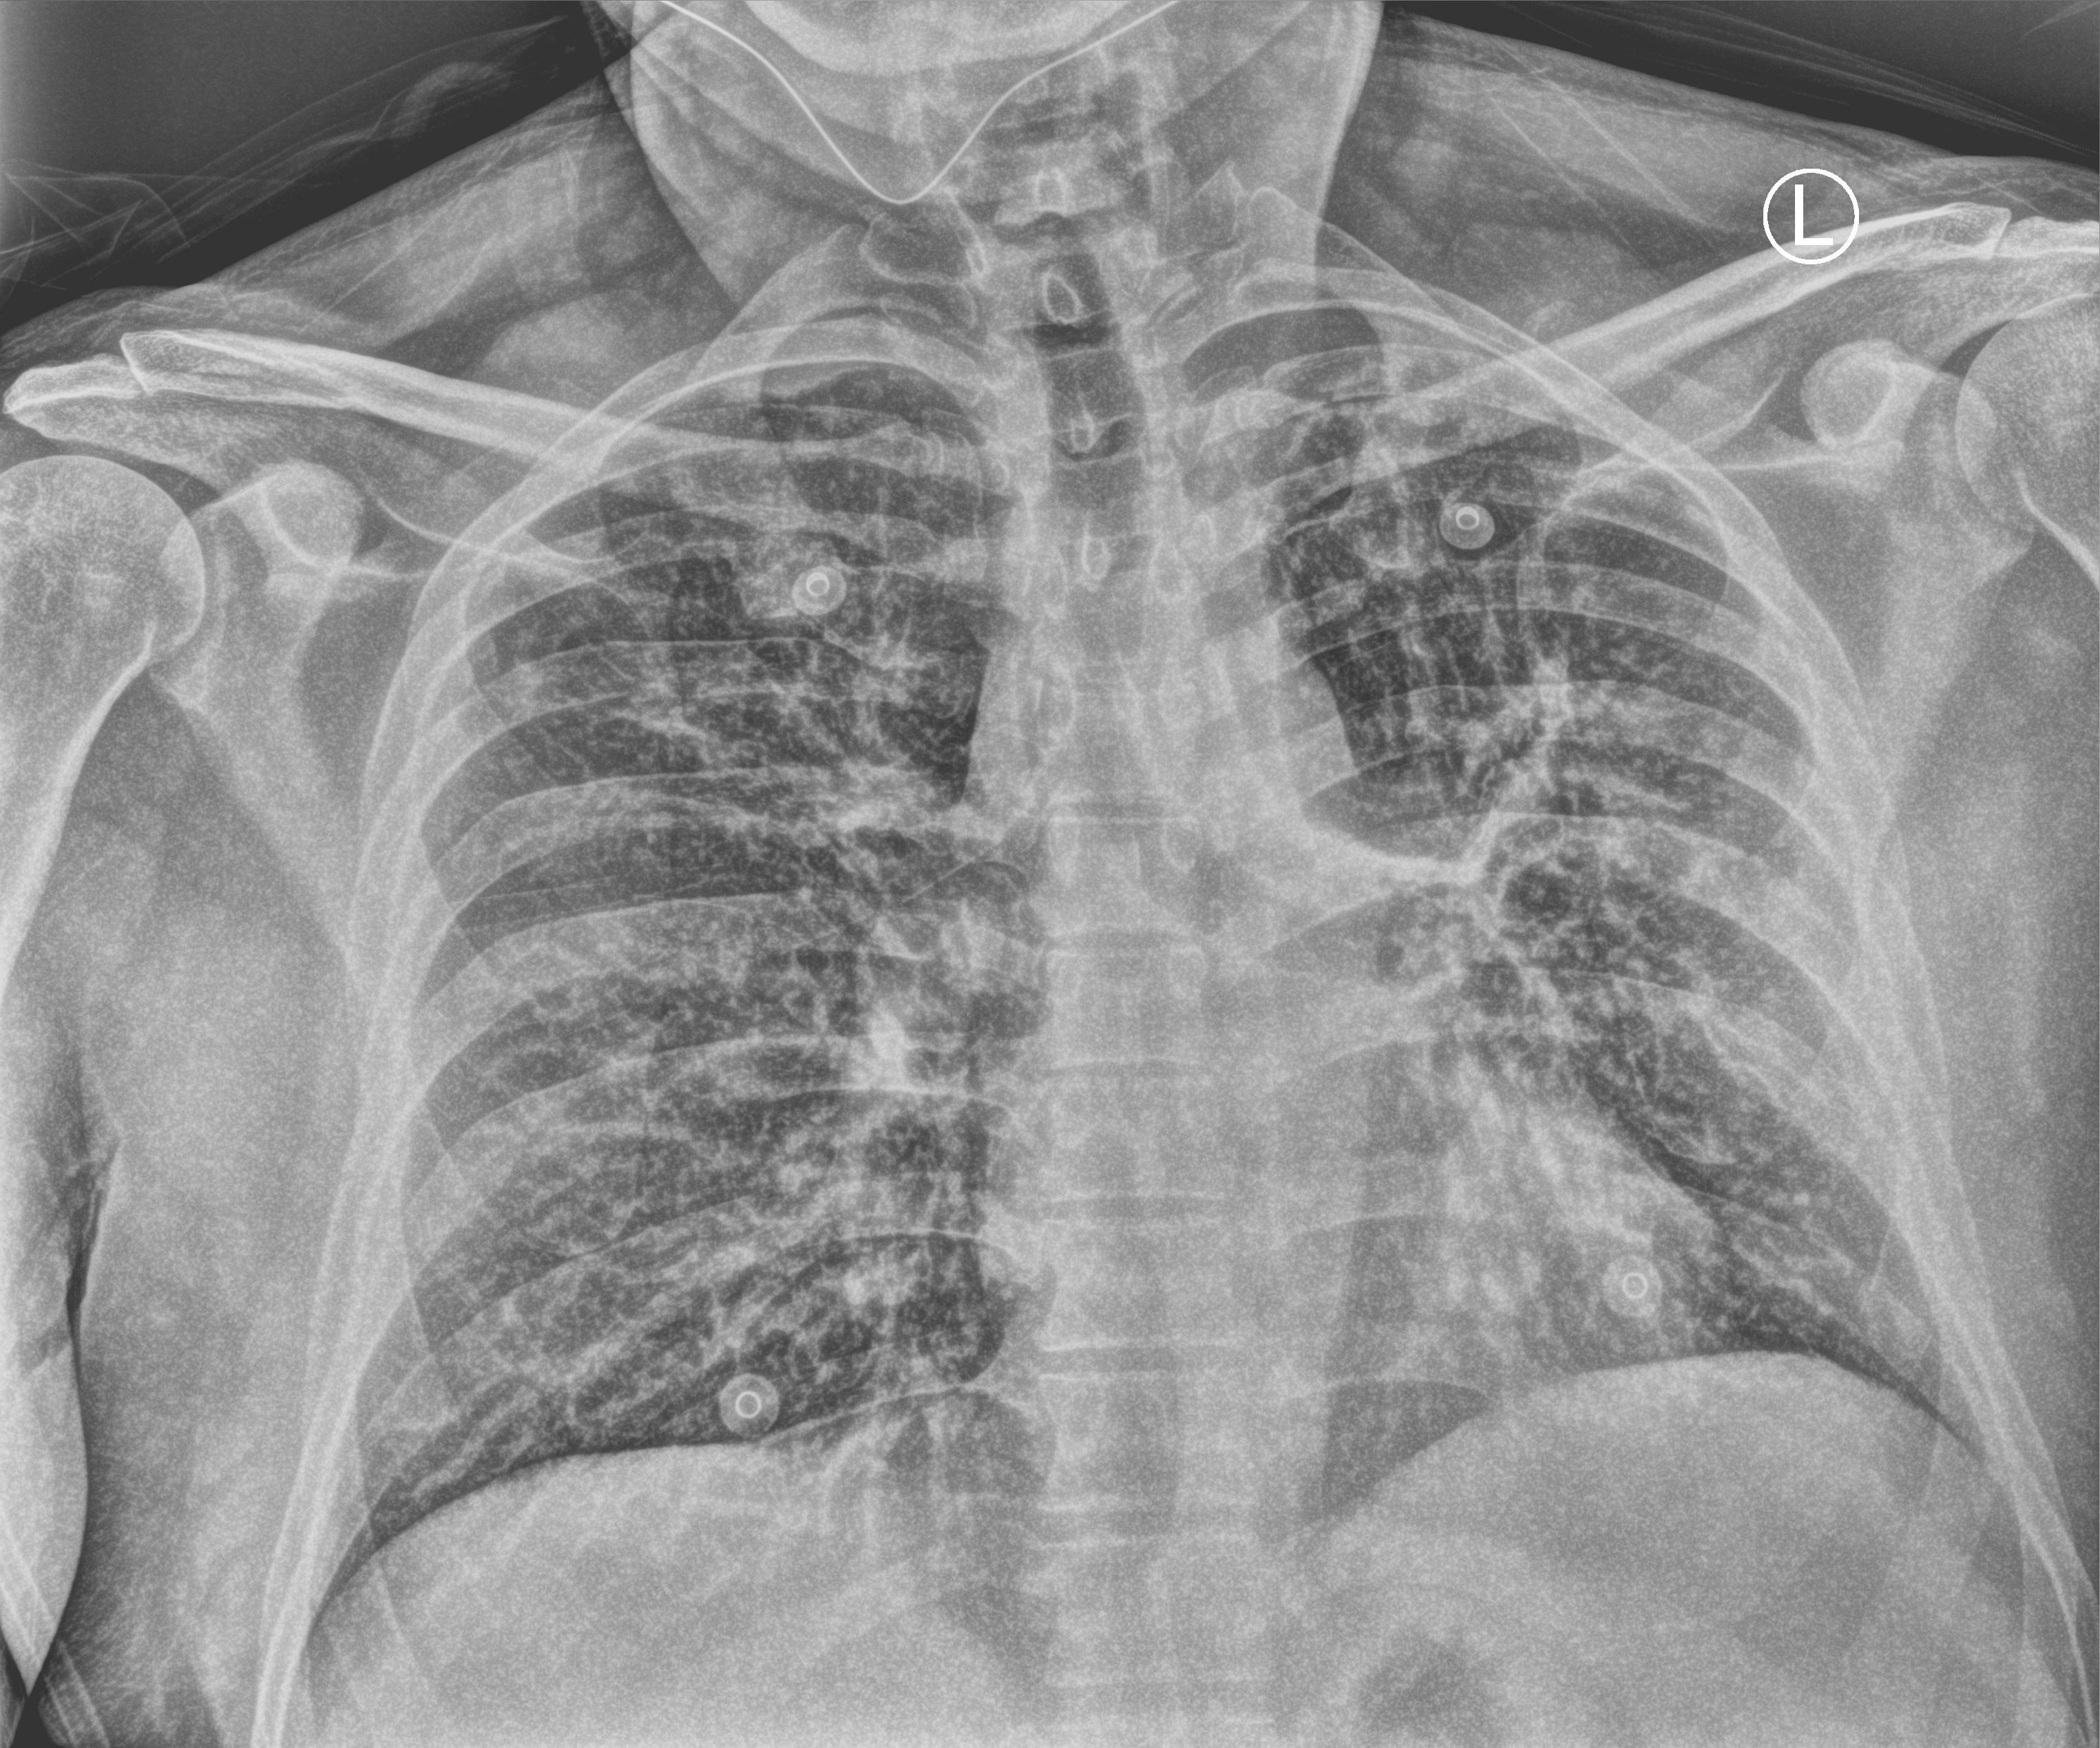
Bedside chest radiograph (computed radiography), anteroposterior (AP) projection. Patient hospitalised with COVID-19; male, aged 18–59 years.
Hospital-stay facts (about this admission, not read from this image; timing relative to this image not recorded):
- length of hospital stay: 2 days
- admitted to intensive care during this hospital stay: no
- mechanically ventilated during this hospital stay: no